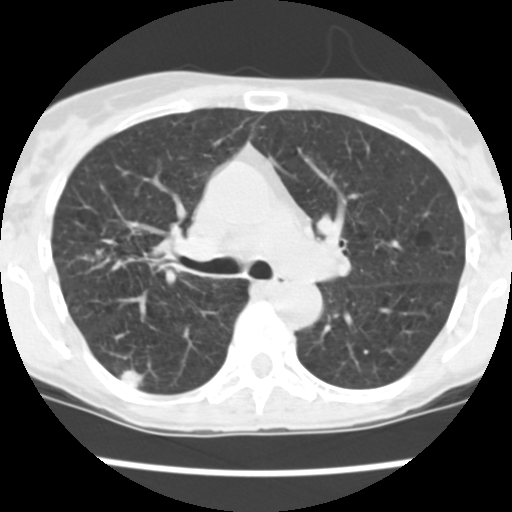
Low-dose screening chest CT, one axial slice. Position 155 of 252 along the scan axis. Reconstruction kernel STANDARD. Lung window (W 1500 / L -600 HU). 2.5 mm slice thickness. 512 × 512 image matrix, field of view 276 × 276 mm.
Outlined on this slice (outlined manually by an expert reader):
- lesion 1 (tumor, upper lobe of right lung): bounding box [x1, y1, x2, y2] px = [121, 369, 143, 389]
- lesion 2 (tumor, lower lobe of right lung): [144, 240, 170, 263]